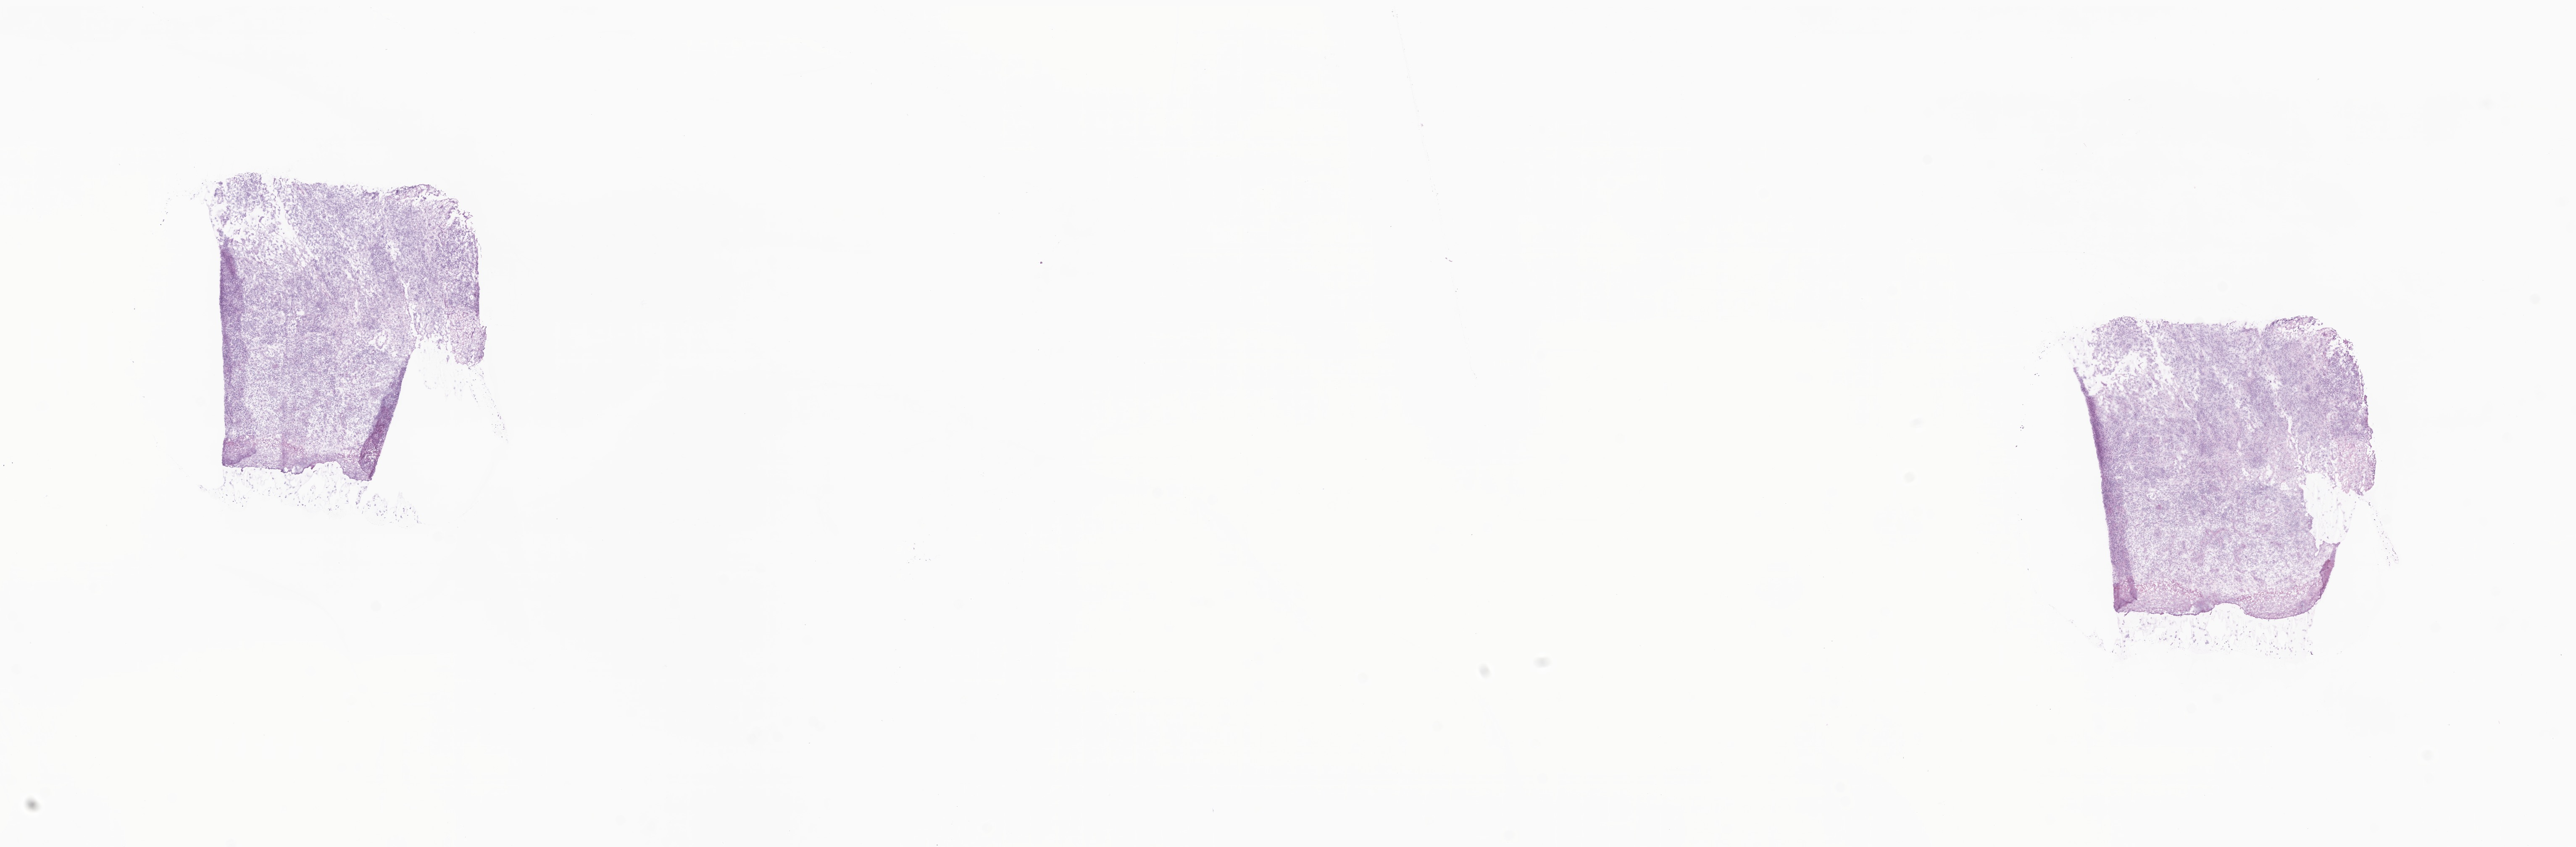
Haematoxylin and eosin whole-slide image, low-resolution overview of the scanned area, about 25.8 x 8.5 mm. Cryosection. Primary tumor. Site: skin. Male patient; age at initial diagnosis 66 years. Composition of this section per pathologist review: tumor cells 80%, tumor nuclei 90%, stromal cells 10%, necrosis 10%, normal cells 0%. Inflammatory infiltration, as recorded: lymphocyte infiltration 0%, monocyte infiltration 0%, neutrophil infiltration 0%.
Histologic diagnosis: Nodular melanoma. AJCC pathologic stage: Stage IIIC. Section: bottom of the tissue portion.